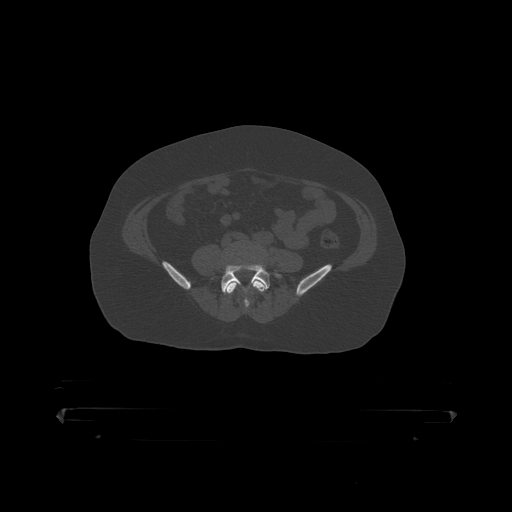
CT including the spine, one axial slice. Slice 49 of 390 in the series (ordered by position). Bone window (W 1800 / L 400 HU). 1.25 mm slice thickness. 512 × 512 image matrix, field of view 650 × 650 mm. Male patient, age 60 years. From the clinical record (not read from this slice): primary cancer: prostate.
Outlined on this slice (semi-automatically segmented with operator editing):
- L4 vertebra: bounding box [x1, y1, x2, y2] px = [226, 254, 267, 310]
- L5 vertebra: [221, 265, 281, 296]